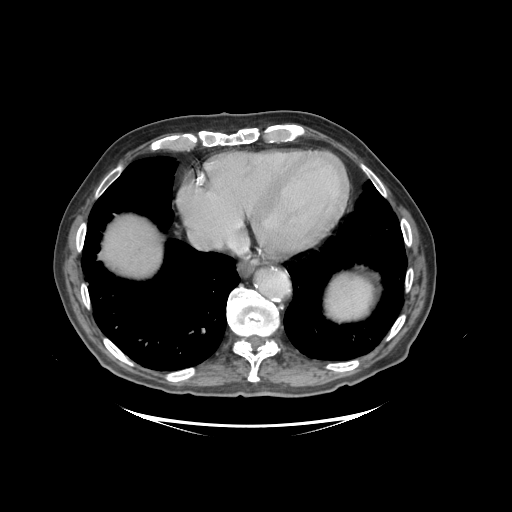
Contrast-enhanced abdominal CT (liver protocol), one axial slice; slice 90 of 99 in the series (ordered by position); reconstruction kernel STANDARD; 140 kVp; soft-tissue window (W 400 / L 40 HU); 2.5 mm slice thickness; 512 × 512 image matrix, field of view 460 × 460 mm. Case-level facts recorded for this patient, not image findings: diagnosis: hepatocellular carcinoma (patient treated with transarterial chemoembolisation; whether this scan precedes or follows treatment is not stated here); TNM stage (as recorded): Stage-I; Child-Pugh class: A; tumour nodularity: uninodular.
Structures marked on this image (semi-automatically segmented with operator editing):
- liver parenchyma outside the tumour (the mass and vessels are separate outlines, so this box may not span the whole liver): bounding box (x1, y1, x2, y2) in pixels: (102, 214, 162, 276)